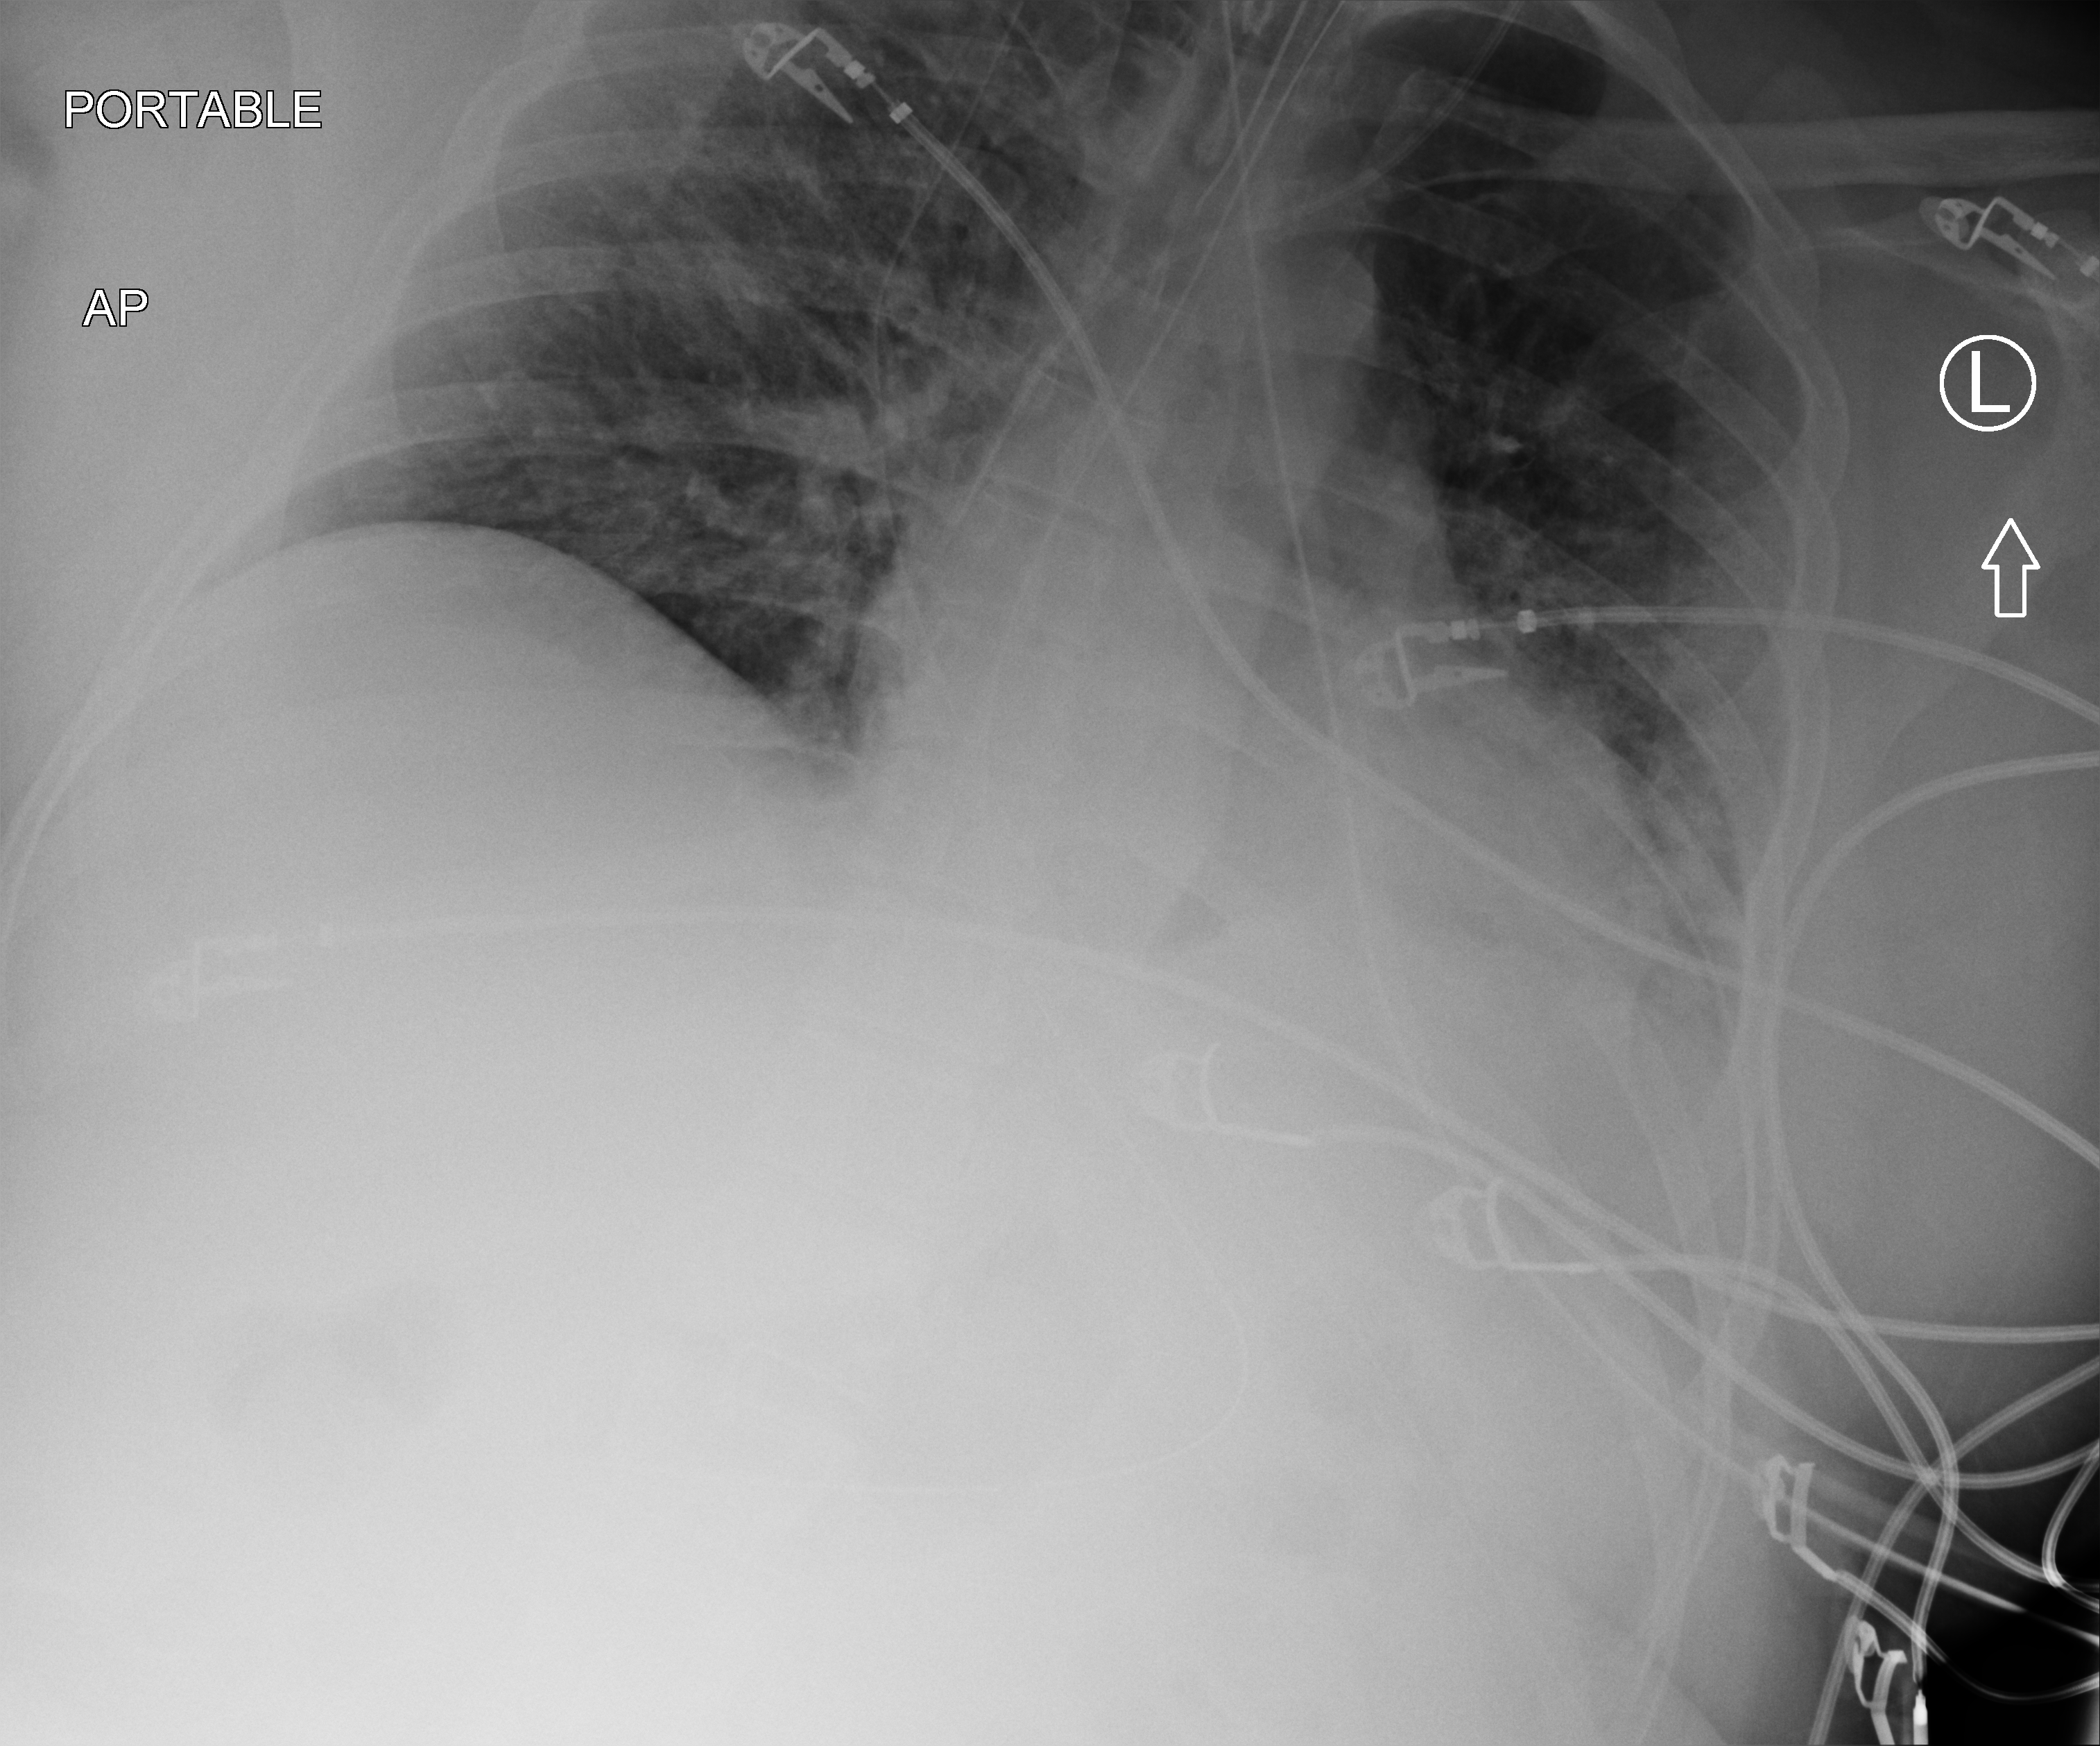
Bedside chest radiograph (computed radiography); anteroposterior (AP) projection. Adult patient hospitalised with COVID-19, age 18–59 years.
Admission-level facts for this patient (not findings on this image; timing relative to this image not recorded):
- diabetes (admission record): no
- length of hospital stay: 16 days
- admitted to intensive care during this hospital stay: yes